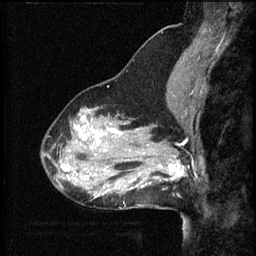
Breast MRI (dynamic contrast-enhanced), one sagittal slice; position 21 of 60 along the scan axis; 3 images stored at this slice position (order not interpretable as contrast timing); 1.5 T; TE 4.2 ms, TR 8.2 ms; 2 mm slice thickness; 256 × 256 image matrix, field of view 200 × 200 mm. Patient: female, 37 years.
Annotated regions visible in this slice (semi-automatically segmented with operator editing):
- analysis volume of interest (the breast-tissue region the enhancement analysis was run in; not a lesion): box from (x=148, y=140) to (x=191, y=191) px
- tumour enhancement mask (voxels above the 70 % enhancement threshold inside the analysis volume of interest): (x=148, y=156)–(x=187, y=185)